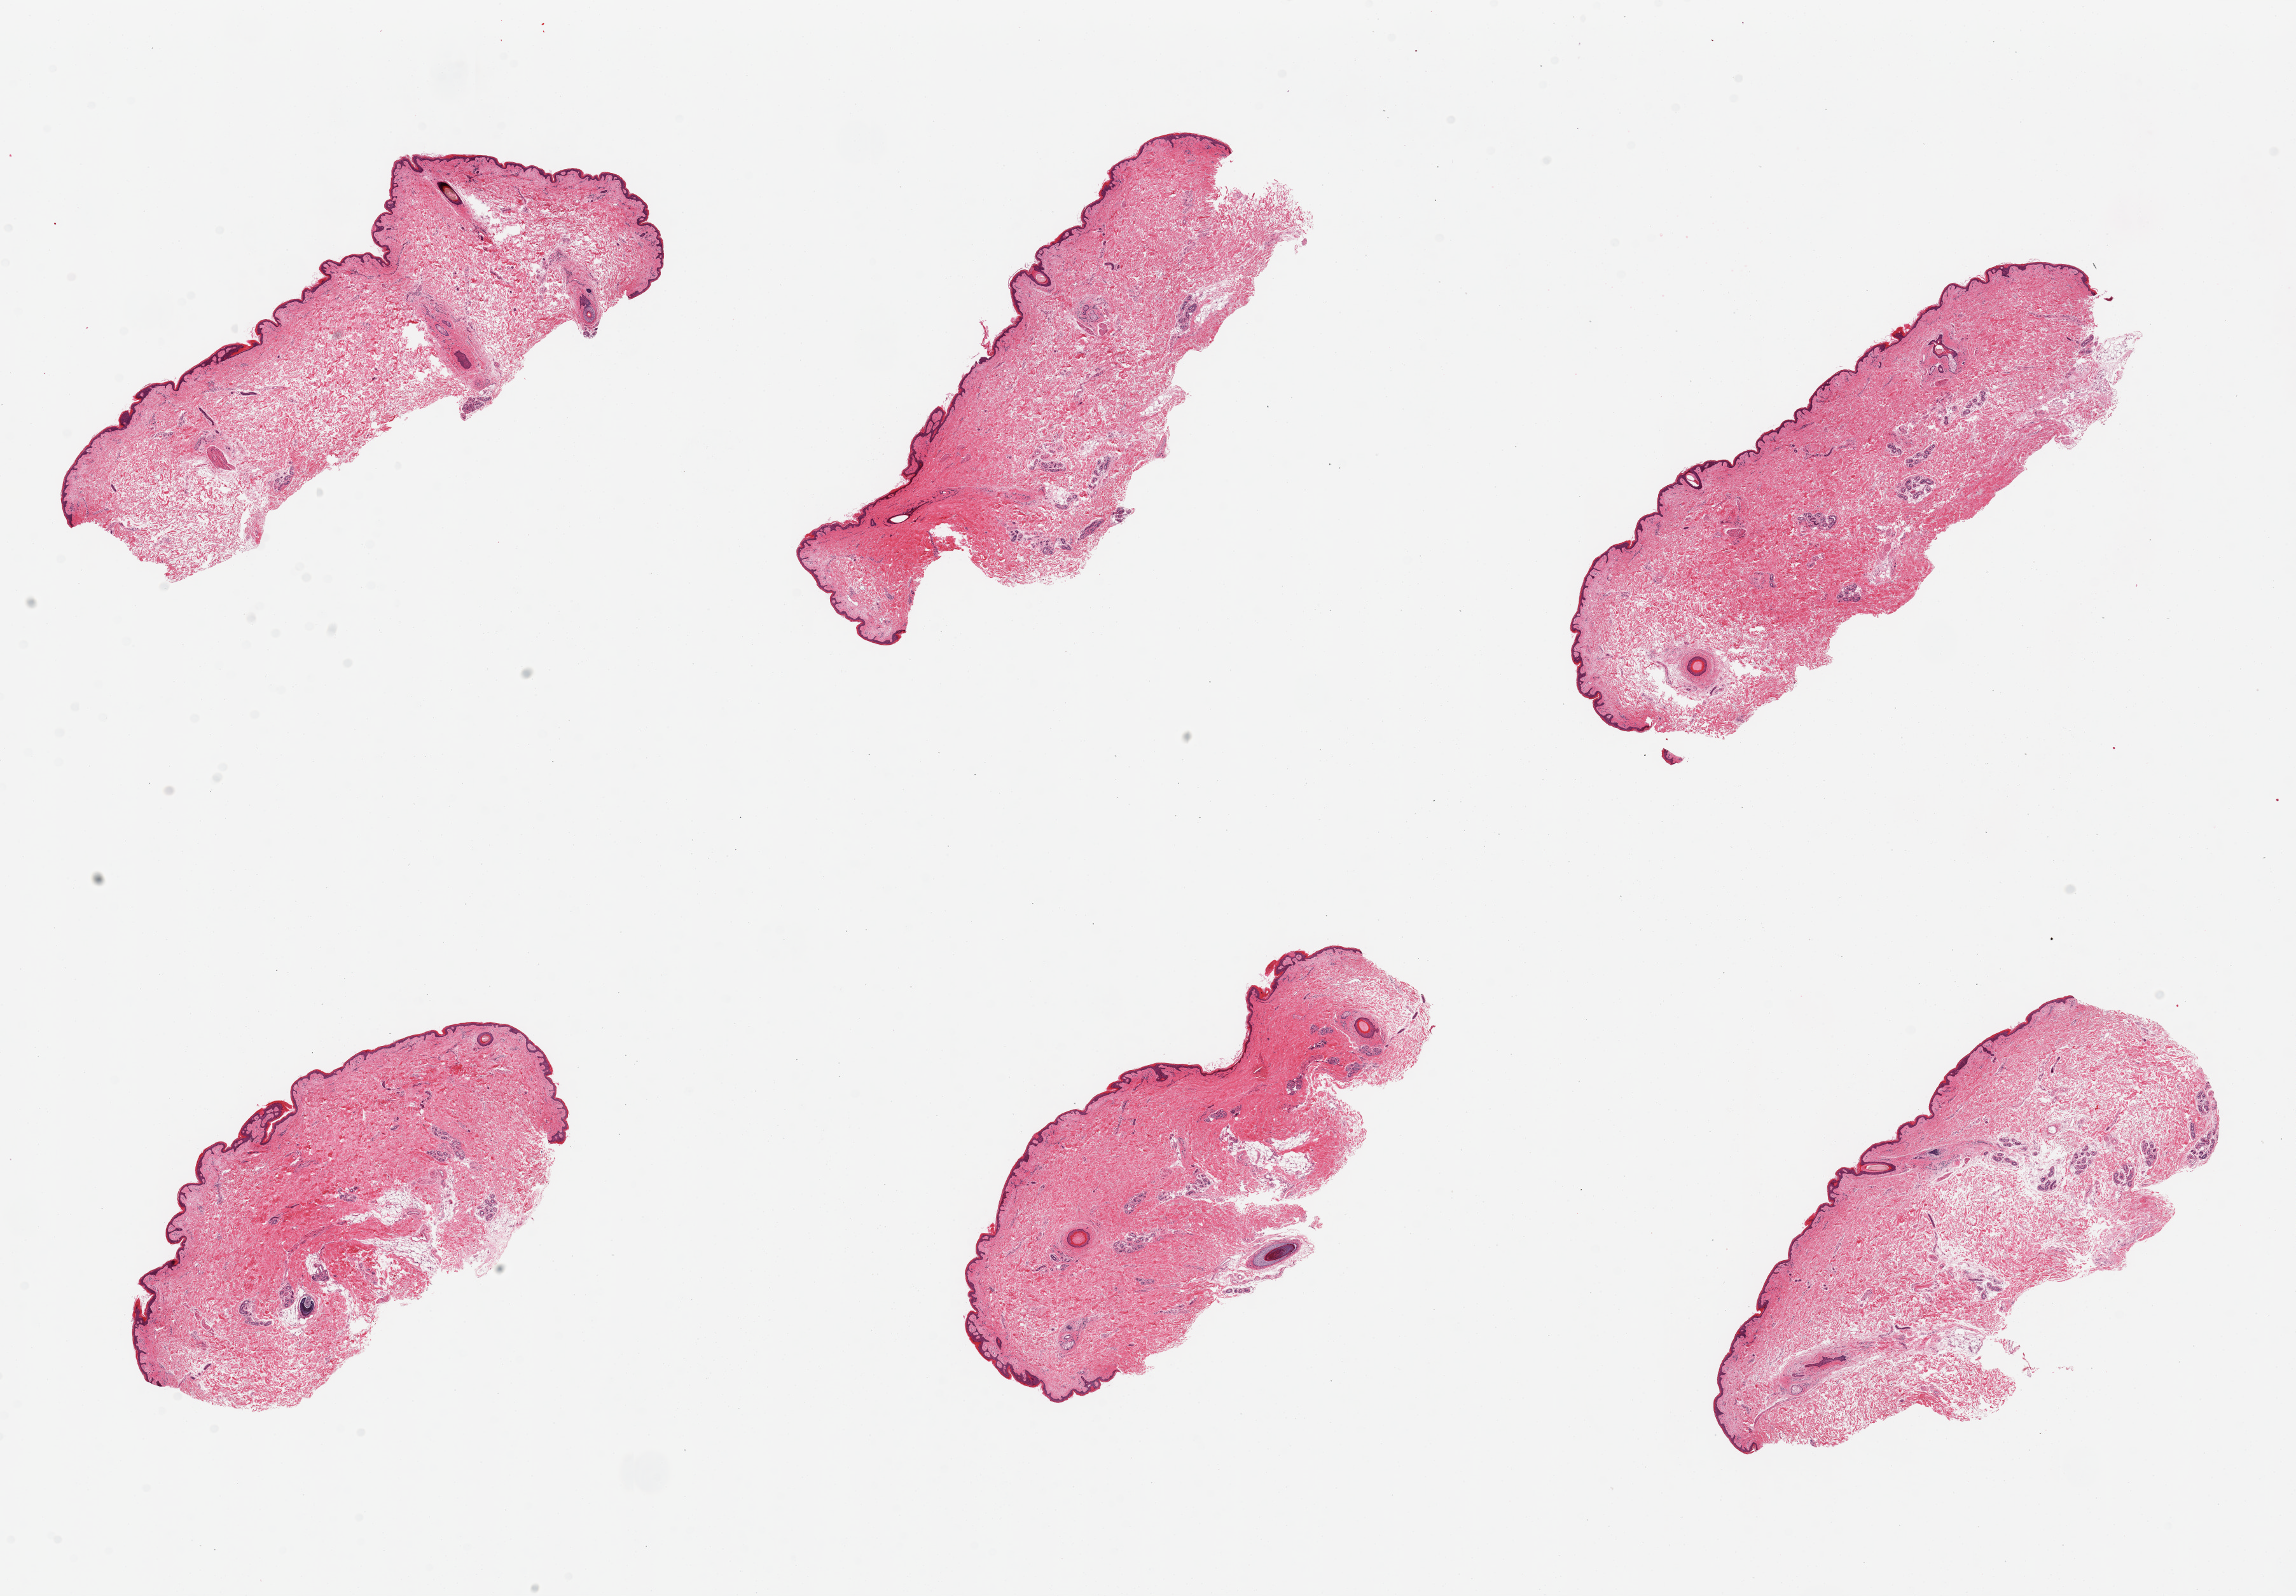
Digitized H&E-stained section, brightfield, a low-resolution overview of the entire scanned area, about 28.5 x 19.8 mm; PAXgene-fixed paraffin-embedded (PFPE) section; sampled site (target tissue): skin of suprapubic region; donor tissue sample. Male donor.
- review note (as recorded): 6 pieces, well trimmed